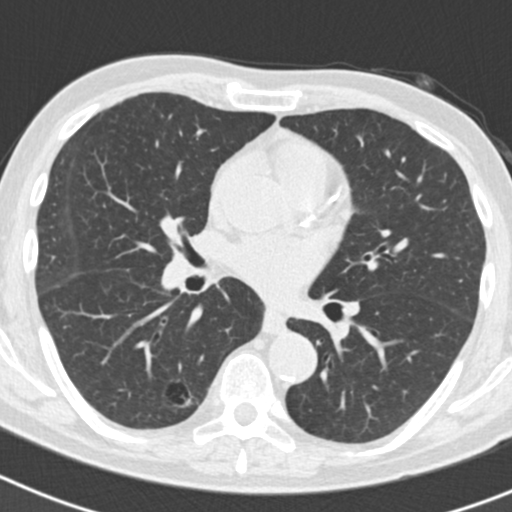
Low-dose screening chest CT, axial slice. Second screening round (one year after baseline). Lung window (W 1500 / L -600 HU). Standard (soft-tissue) reconstruction kernel (B30f). Slice 86 of 186 in the series. Male participant, aged 70 years at enrolment.
- Expert reader's lesion annotation, bounding box <129,367,203,432> (left, top, right, bottom; pixels).
- The screening reader recorded 5 non-calcified nodules or masses ≥4 mm on this exam (right lower lobe, right lower lobe, right upper lobe, right upper lobe, left upper lobe); which of them this box marks is not recorded.
- Later outcome: lung cancer diagnosed 622 days after this screen — bronchiolo-alveolar adenocarcinoma, NOS, right lower lobe, poorly differentiated (G3), stage IB (AJCC 6th edition), 30 mm at pathology.